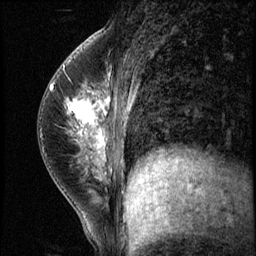
Breast MRI (dynamic contrast-enhanced), one sagittal slice; position 27 of 56 along the scan axis; 3 images stored at this slice position (order not interpretable as contrast timing); 1.5 T; TE 4.2 ms, TR 8.7 ms; 2.5 mm slice thickness; 256 × 256 image matrix, field of view 180 × 180 mm. Female patient, age 35 years. From the clinical record (not read from this slice): setting: breast cancer imaged before/during neoadjuvant chemotherapy; receptor status: HER2-positive.
Structures marked on this image (semi-automatically segmented with operator editing):
- analysis volume of interest (the breast-tissue region the enhancement analysis was run in; not a lesion): bounding box [x1, y1, x2, y2] px = [58, 84, 138, 186]
- tumour enhancement mask (voxels above the 140 % enhancement threshold inside the analysis volume of interest): [66, 97, 109, 160]